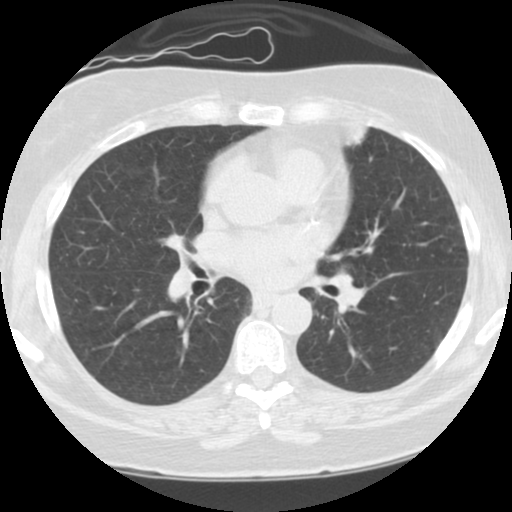
Low-dose screening chest CT, one axial slice; slice 58 of 108 in the series (ordered by position); reconstruction kernel STANDARD; lung window (W 1500 / L -600 HU); 2.5 mm slice thickness; 512 × 512 image matrix.
Outlined on this slice (outlined manually by an expert reader):
- lesion 1 (tumor, hilum of left lung): bounding box [x1, y1, x2, y2] px = [330, 273, 365, 306]